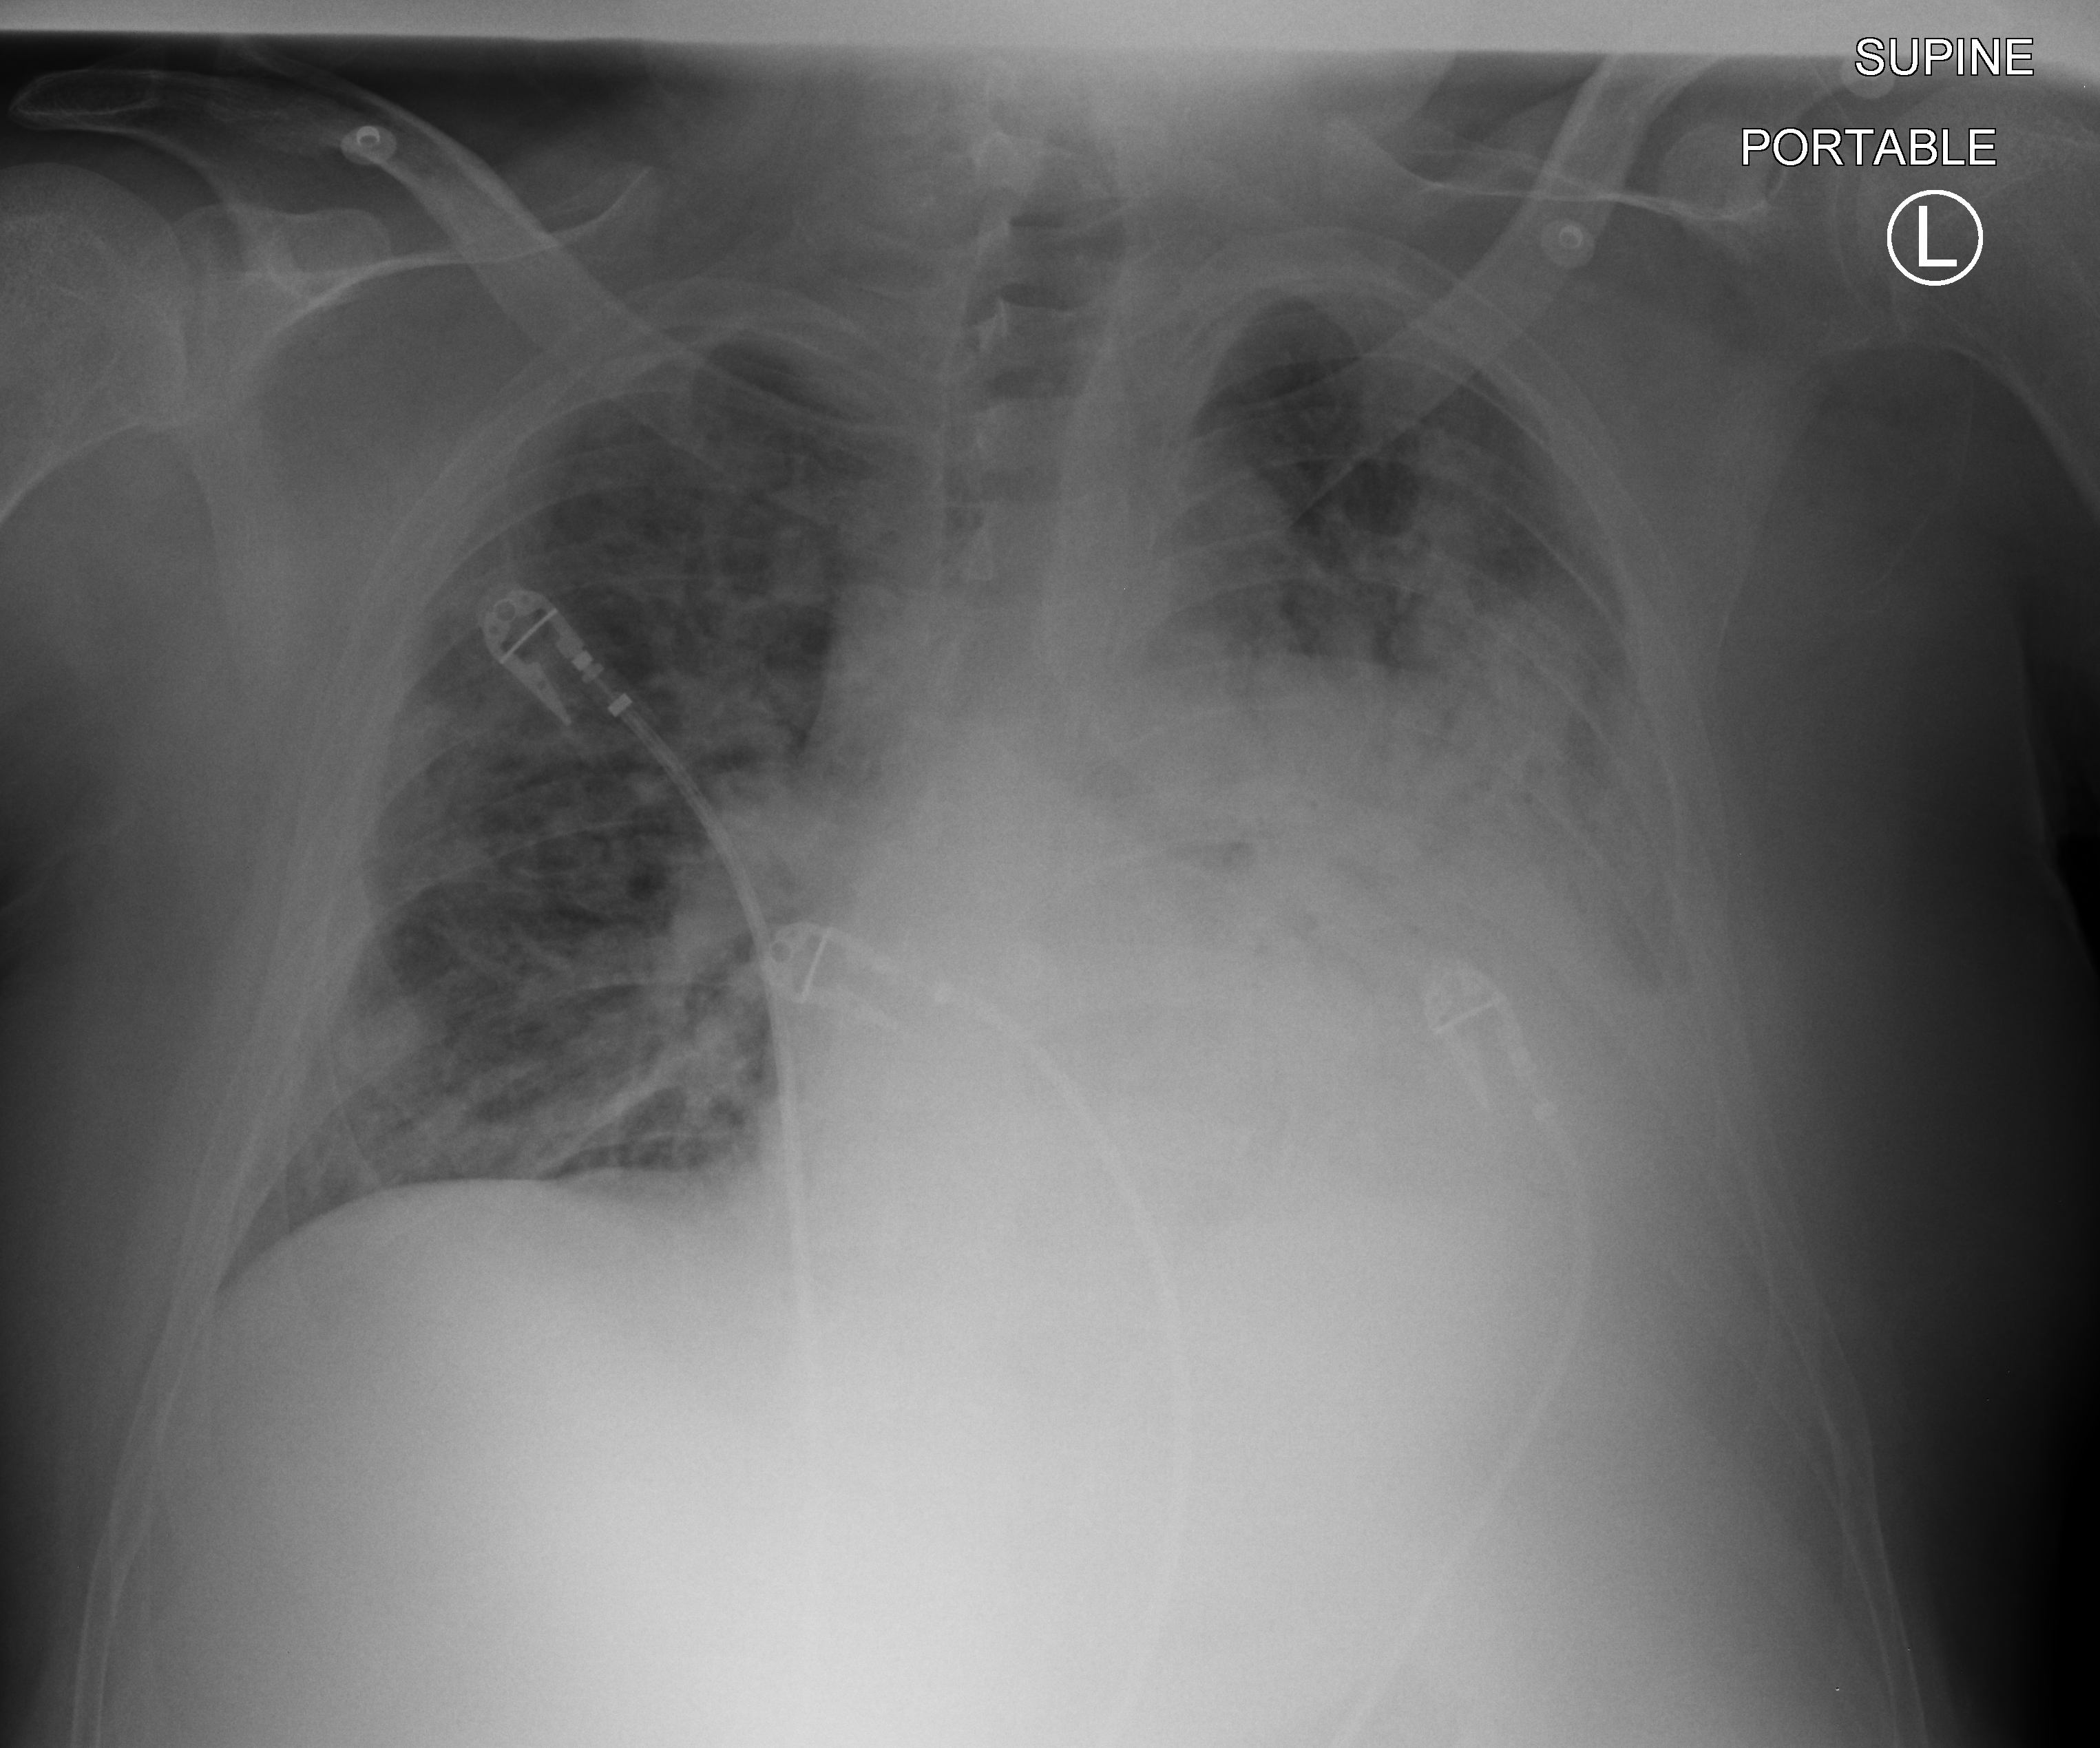
Chest X-ray (portable). Patient hospitalised with COVID-19; male, aged 18–59 years.
Admission-level facts for this patient (not findings on this image; timing relative to this image not recorded): admitted to intensive care during this hospital stay: no.